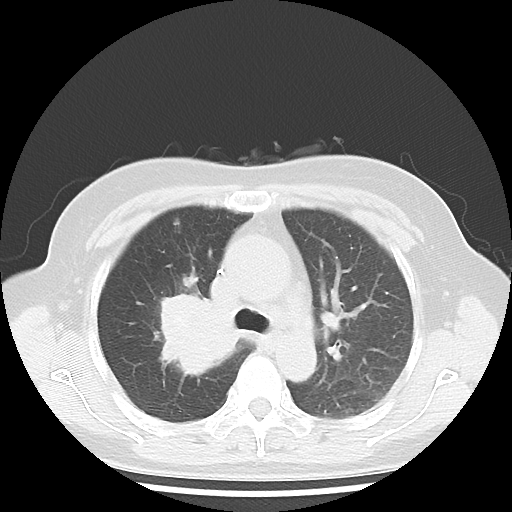
Chest CT, one axial slice. Position 28 of 43 along the scan axis. Reconstruction kernel LUNG. 100 kVp. Lung window (W 1500 / L -600 HU). 5 mm slice thickness. 512 × 512 image matrix, field of view 316 × 316 mm. Patient: female, 62 years. Case-level facts recorded for this patient, not image findings: clinical TNM (as recorded): T3 N0 M0; histopathological grade: G3.
Outlined on this slice (rectangle marked by the reading radiologist):
- lung tumour (recorded histology: small cell carcinoma): bounding box [x1, y1, x2, y2] px = [133, 282, 242, 397]